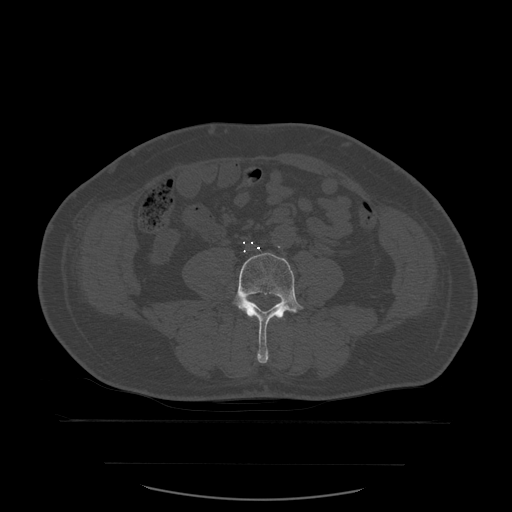
CT including the spine, one axial slice. Slice 165 of 590 in the series (ordered by position). Bone window (W 1800 / L 400 HU). 1.25 mm slice thickness. 512 × 512 image matrix, field of view 479 × 479 mm. Patient age 71 years. From the clinical record (not read from this slice): primary cancer: lung.
Structures marked on this image (semi-automatic segmentation, software-assisted and operator-edited):
- L4 vertebra: bounding box [x1, y1, x2, y2] px = [211, 253, 304, 364]